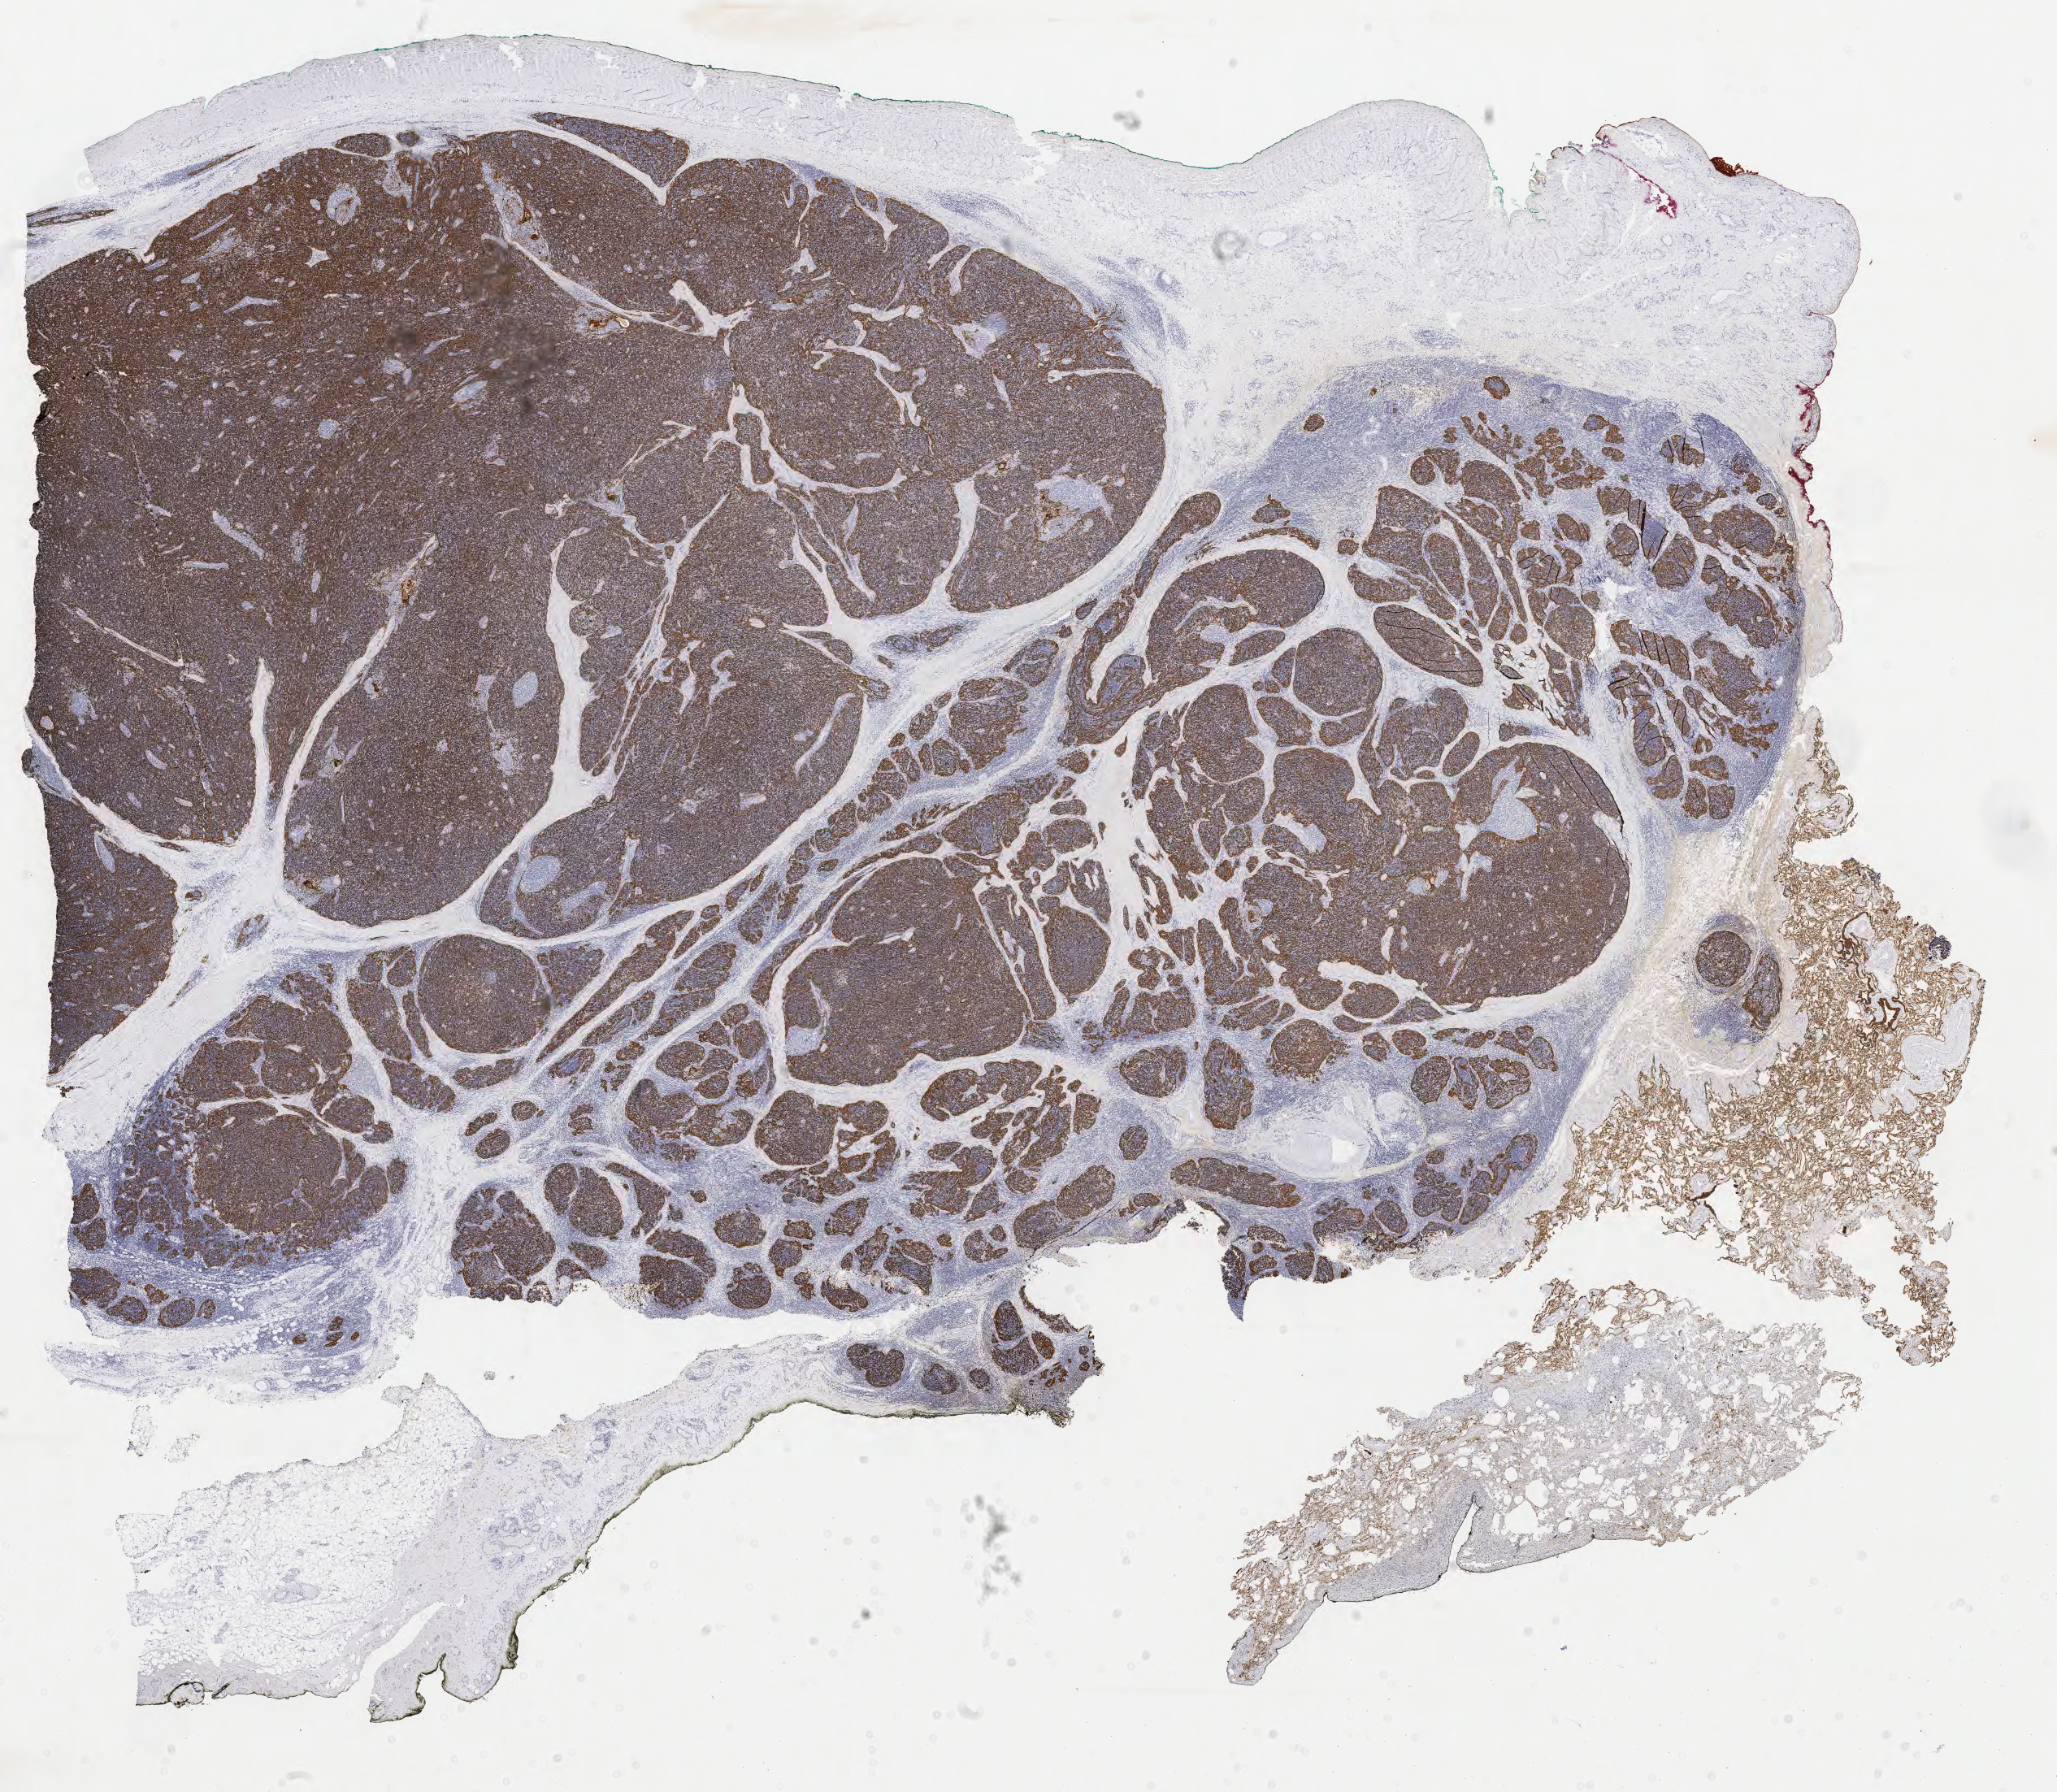
Digitized H&E-stained tissue section (whole slide) — low-resolution overview of the scanned area, about 20.1 x 17.5 mm (slide scanned at 40x). Formalin-fixed paraffin-embedded (FFPE) diagnostic section. Thymus, primary tumour sample. Female patient; age at initial diagnosis 57 years.
• diagnosis: Thymoma, type B1, NOS